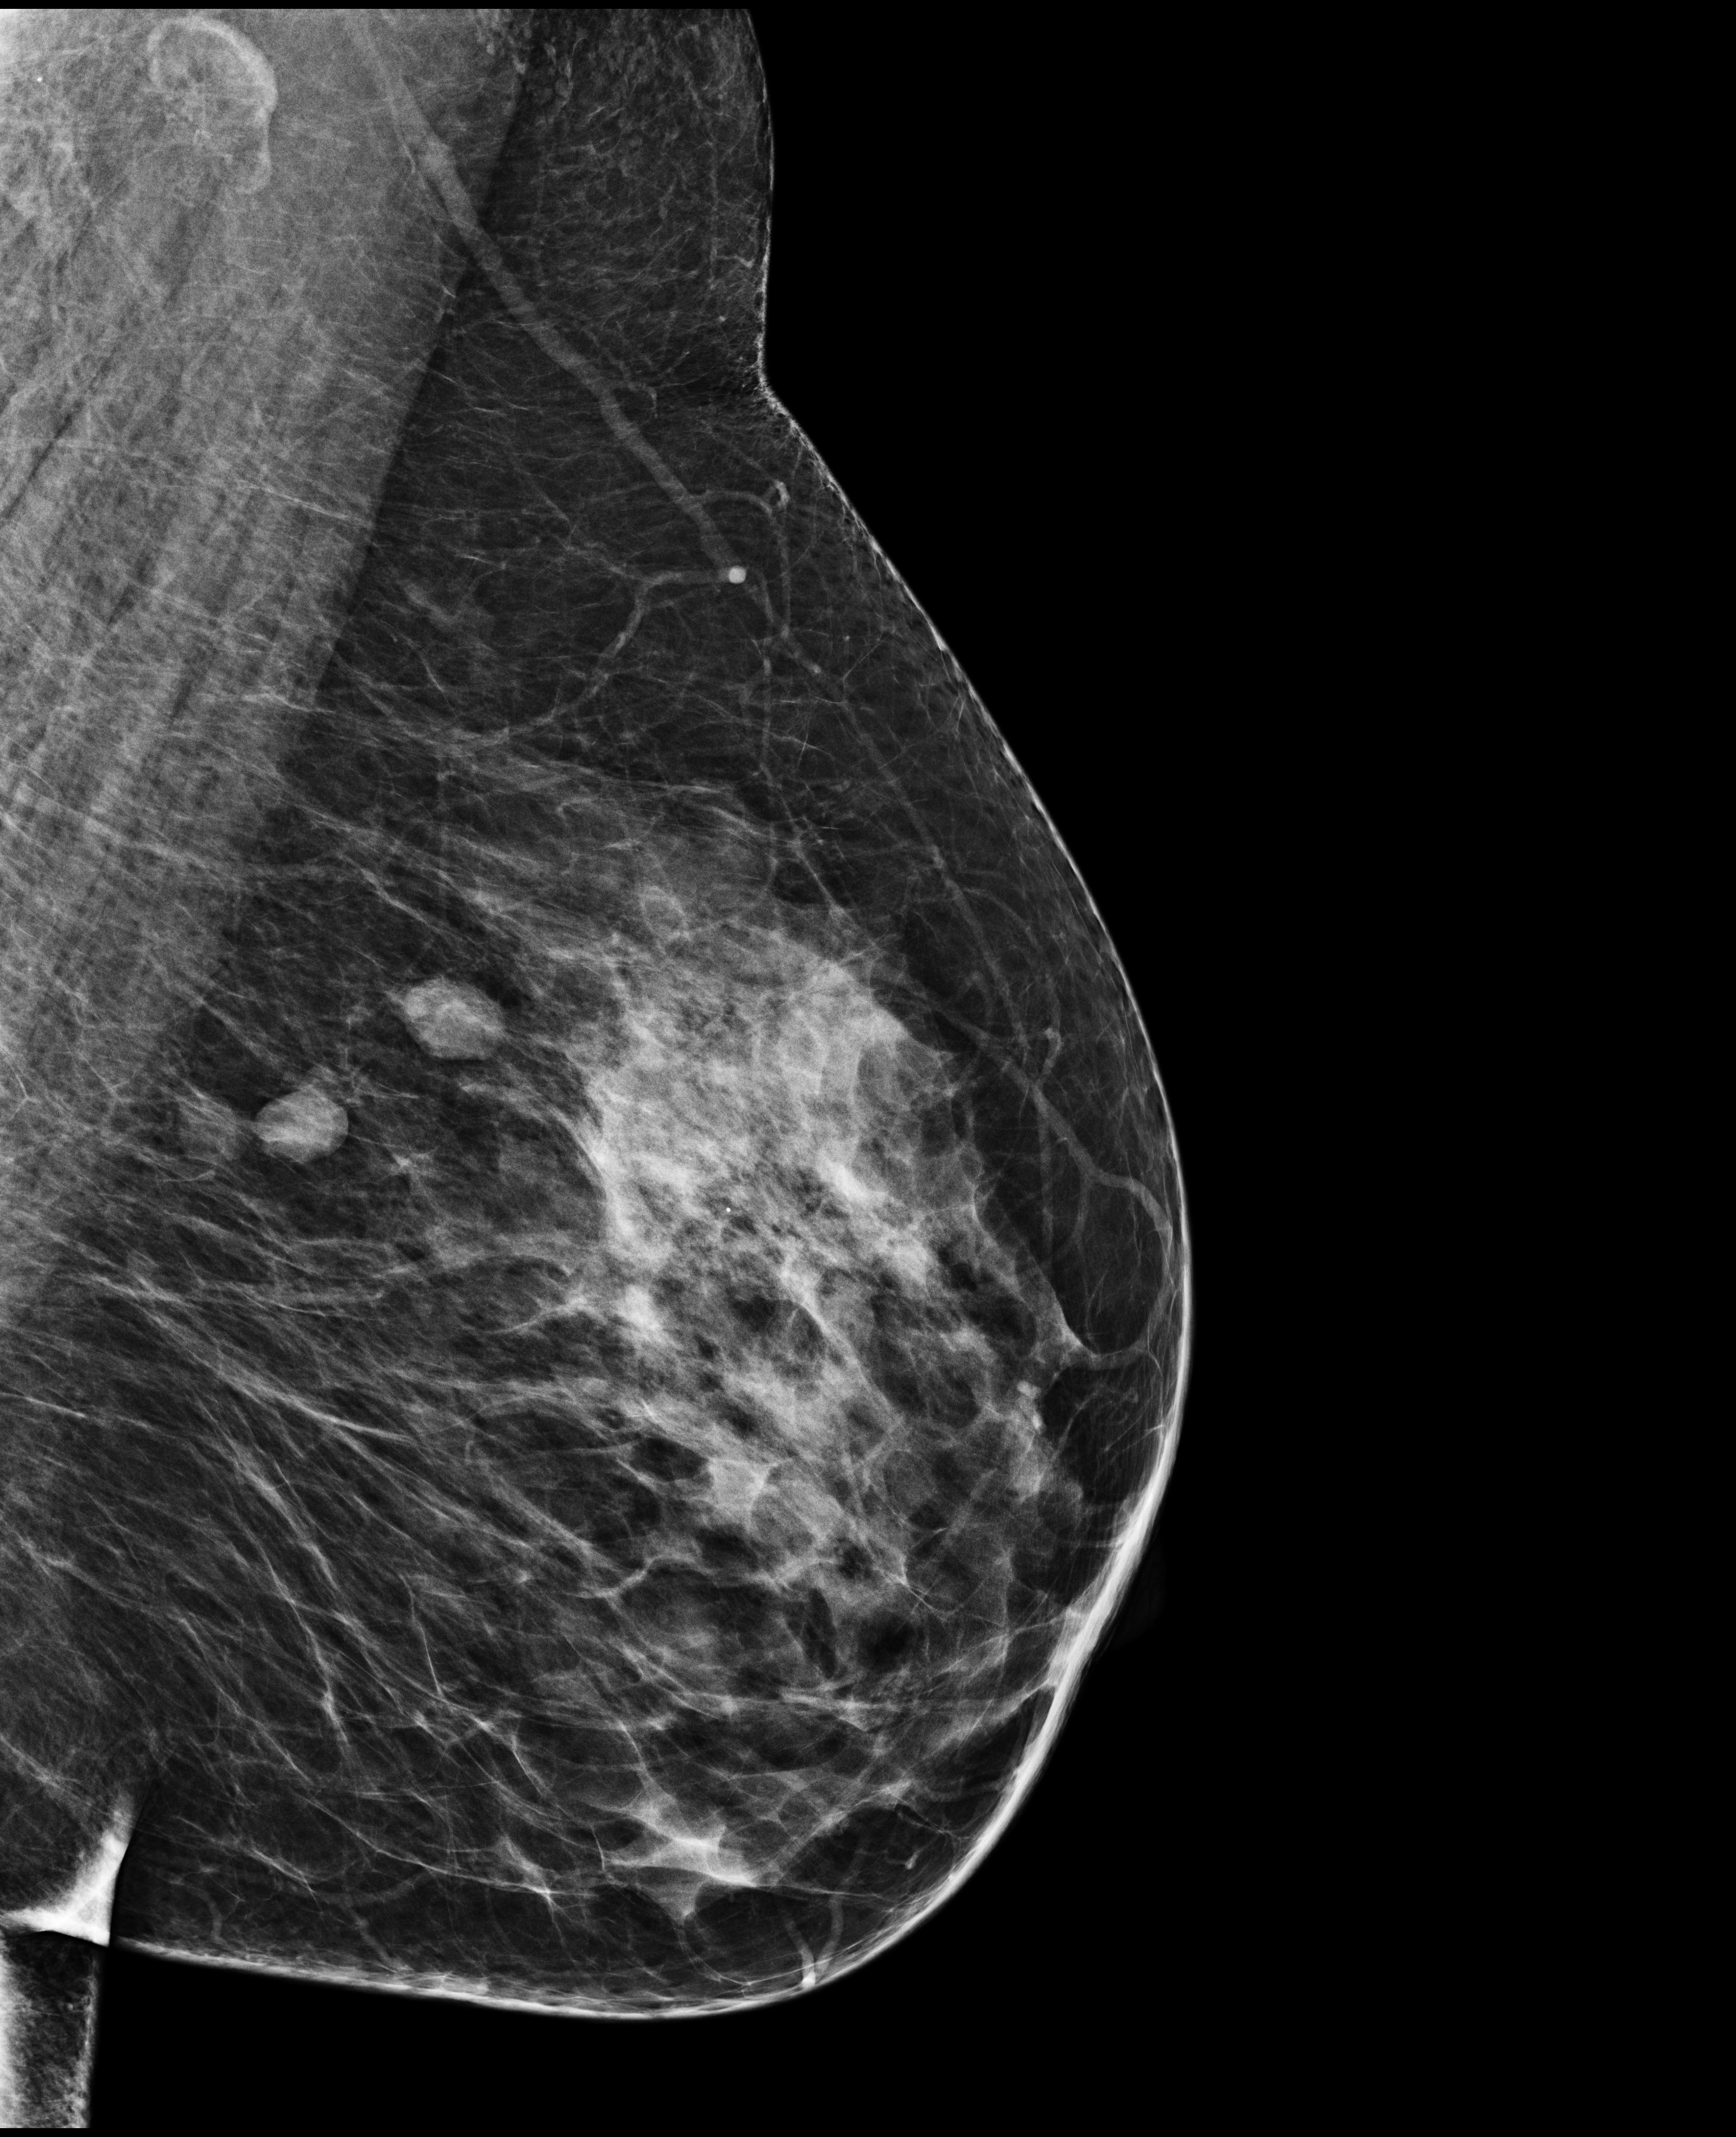
Digital mammogram (FFDM), left breast, MLO view, annual screening mammography examination, compressed breast thickness 69 mm. Patient: female, 48 years.
BI-RADS breast density category at the screening exam (both breasts, scale 1–4): 3. Final BI-RADS assessment for this screening round (tomosynthesis exam, both breasts): category 2. Recall: no recall after this screen.